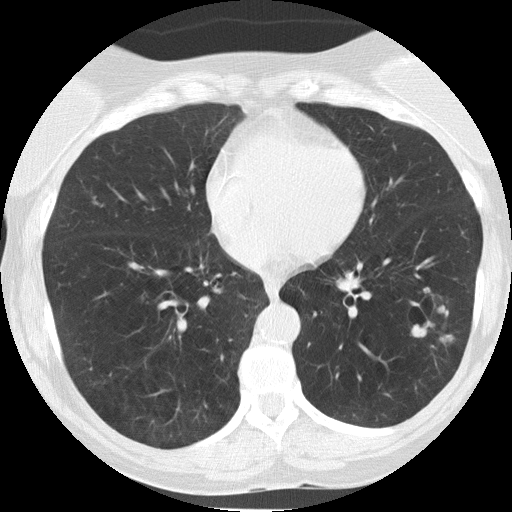
Axial slice from a low-dose chest CT screening exam; baseline annual screen; lung window (W 1500 / L -600 HU); 2 mm slice thickness; 120 kVp; slice 86 of 149 in the series; 512 × 512 image matrix, field of view 290 × 290 mm. Female participant, aged 58 years at enrolment. Current smoker at enrolment.
Lesion marked by an expert reader, box from (x=406, y=303) to (x=457, y=347) px. The screening reader recorded 3 non-calcified nodules or masses ≥4 mm on this exam (right lower lobe, lingula, left lower lobe); which of them this box marks is not recorded. Official screen result: positive, change unspecified: nodule(s) >= 4 mm or enlarging nodule(s), mass(es), or other non-specific abnormalities suspicious for lung cancer. Lung cancer was diagnosed 93 days after this screen: adenocarcinoma, NOS, left lower lobe, moderately differentiated (G2), stage IIIB (AJCC 6th edition), 14 mm at pathology.